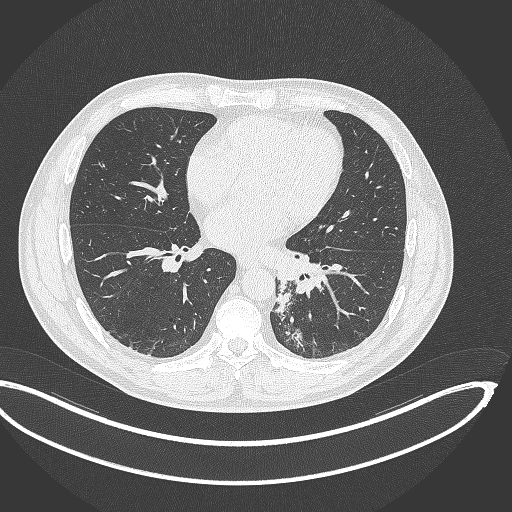
Chest CT, one axial slice; position 152 of 362 along the scan axis; reconstruction kernel B70f; 120 kVp; lung window (W 1500 / L -600 HU); 1 mm slice thickness; 512 × 512 image matrix, field of view 442 × 442 mm. Male patient, age 50 years. From the clinical record (not read from this slice): clinical TNM (as recorded): T2a N3 M0.
Structures marked on this image (bounding box drawn by a radiologist):
- lung tumour (recorded histology: squamous cell carcinoma): bounding box (x1, y1, x2, y2) in pixels: (274, 280, 295, 314)